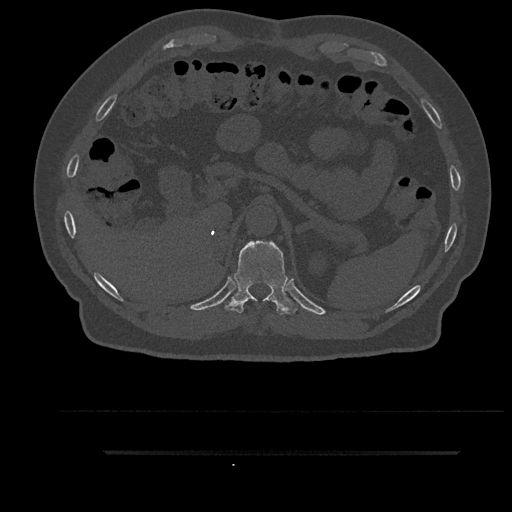
CT including the spine, one axial slice. Slice 316 of 797 in the series (ordered by position). 120 kVp. Bone window (W 1800 / L 400 HU). 0.5 mm slice thickness. 512 × 512 image matrix. Patient: male, 63 years. From the clinical record (not read from this slice): primary cancer: renal.
Structures marked on this image (semi-automatically segmented with operator editing):
- T11 vertebra: box from (x=225, y=241) to (x=297, y=315) px